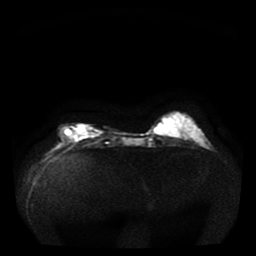
Breast MRI, one axial slice. Slice 10 of 36 in the series (ordered by position). Diffusion-weighted series; image 2 of 4 stored at this slice position (different b-values; order by instance number). 1.5 T. 256 × 256 image matrix. Female patient.
Annotated regions visible in this slice (outlined manually by an expert reader):
- tumour on diffusion-weighted imaging: box from (x=63, y=125) to (x=85, y=135) px